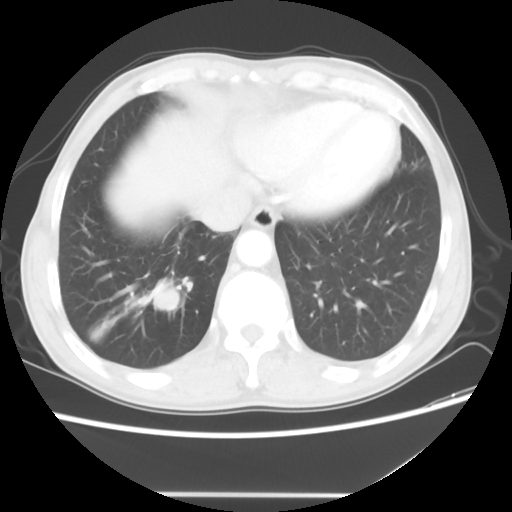
Chest CT, one axial slice; slice 11 of 56 in the series (ordered by position); 120 kVp; lung window (W 1500 / L -600 HU); 512 × 512 image matrix, field of view 344 × 344 mm. Patient: male, 65 years. Case-level facts recorded for this patient, not image findings: clinical TNM (as recorded): T1c N3 M0.
Structures marked on this image (bounding box drawn by a radiologist):
- lung tumour (recorded histology: small cell carcinoma): box from (x=135, y=277) to (x=180, y=318) px